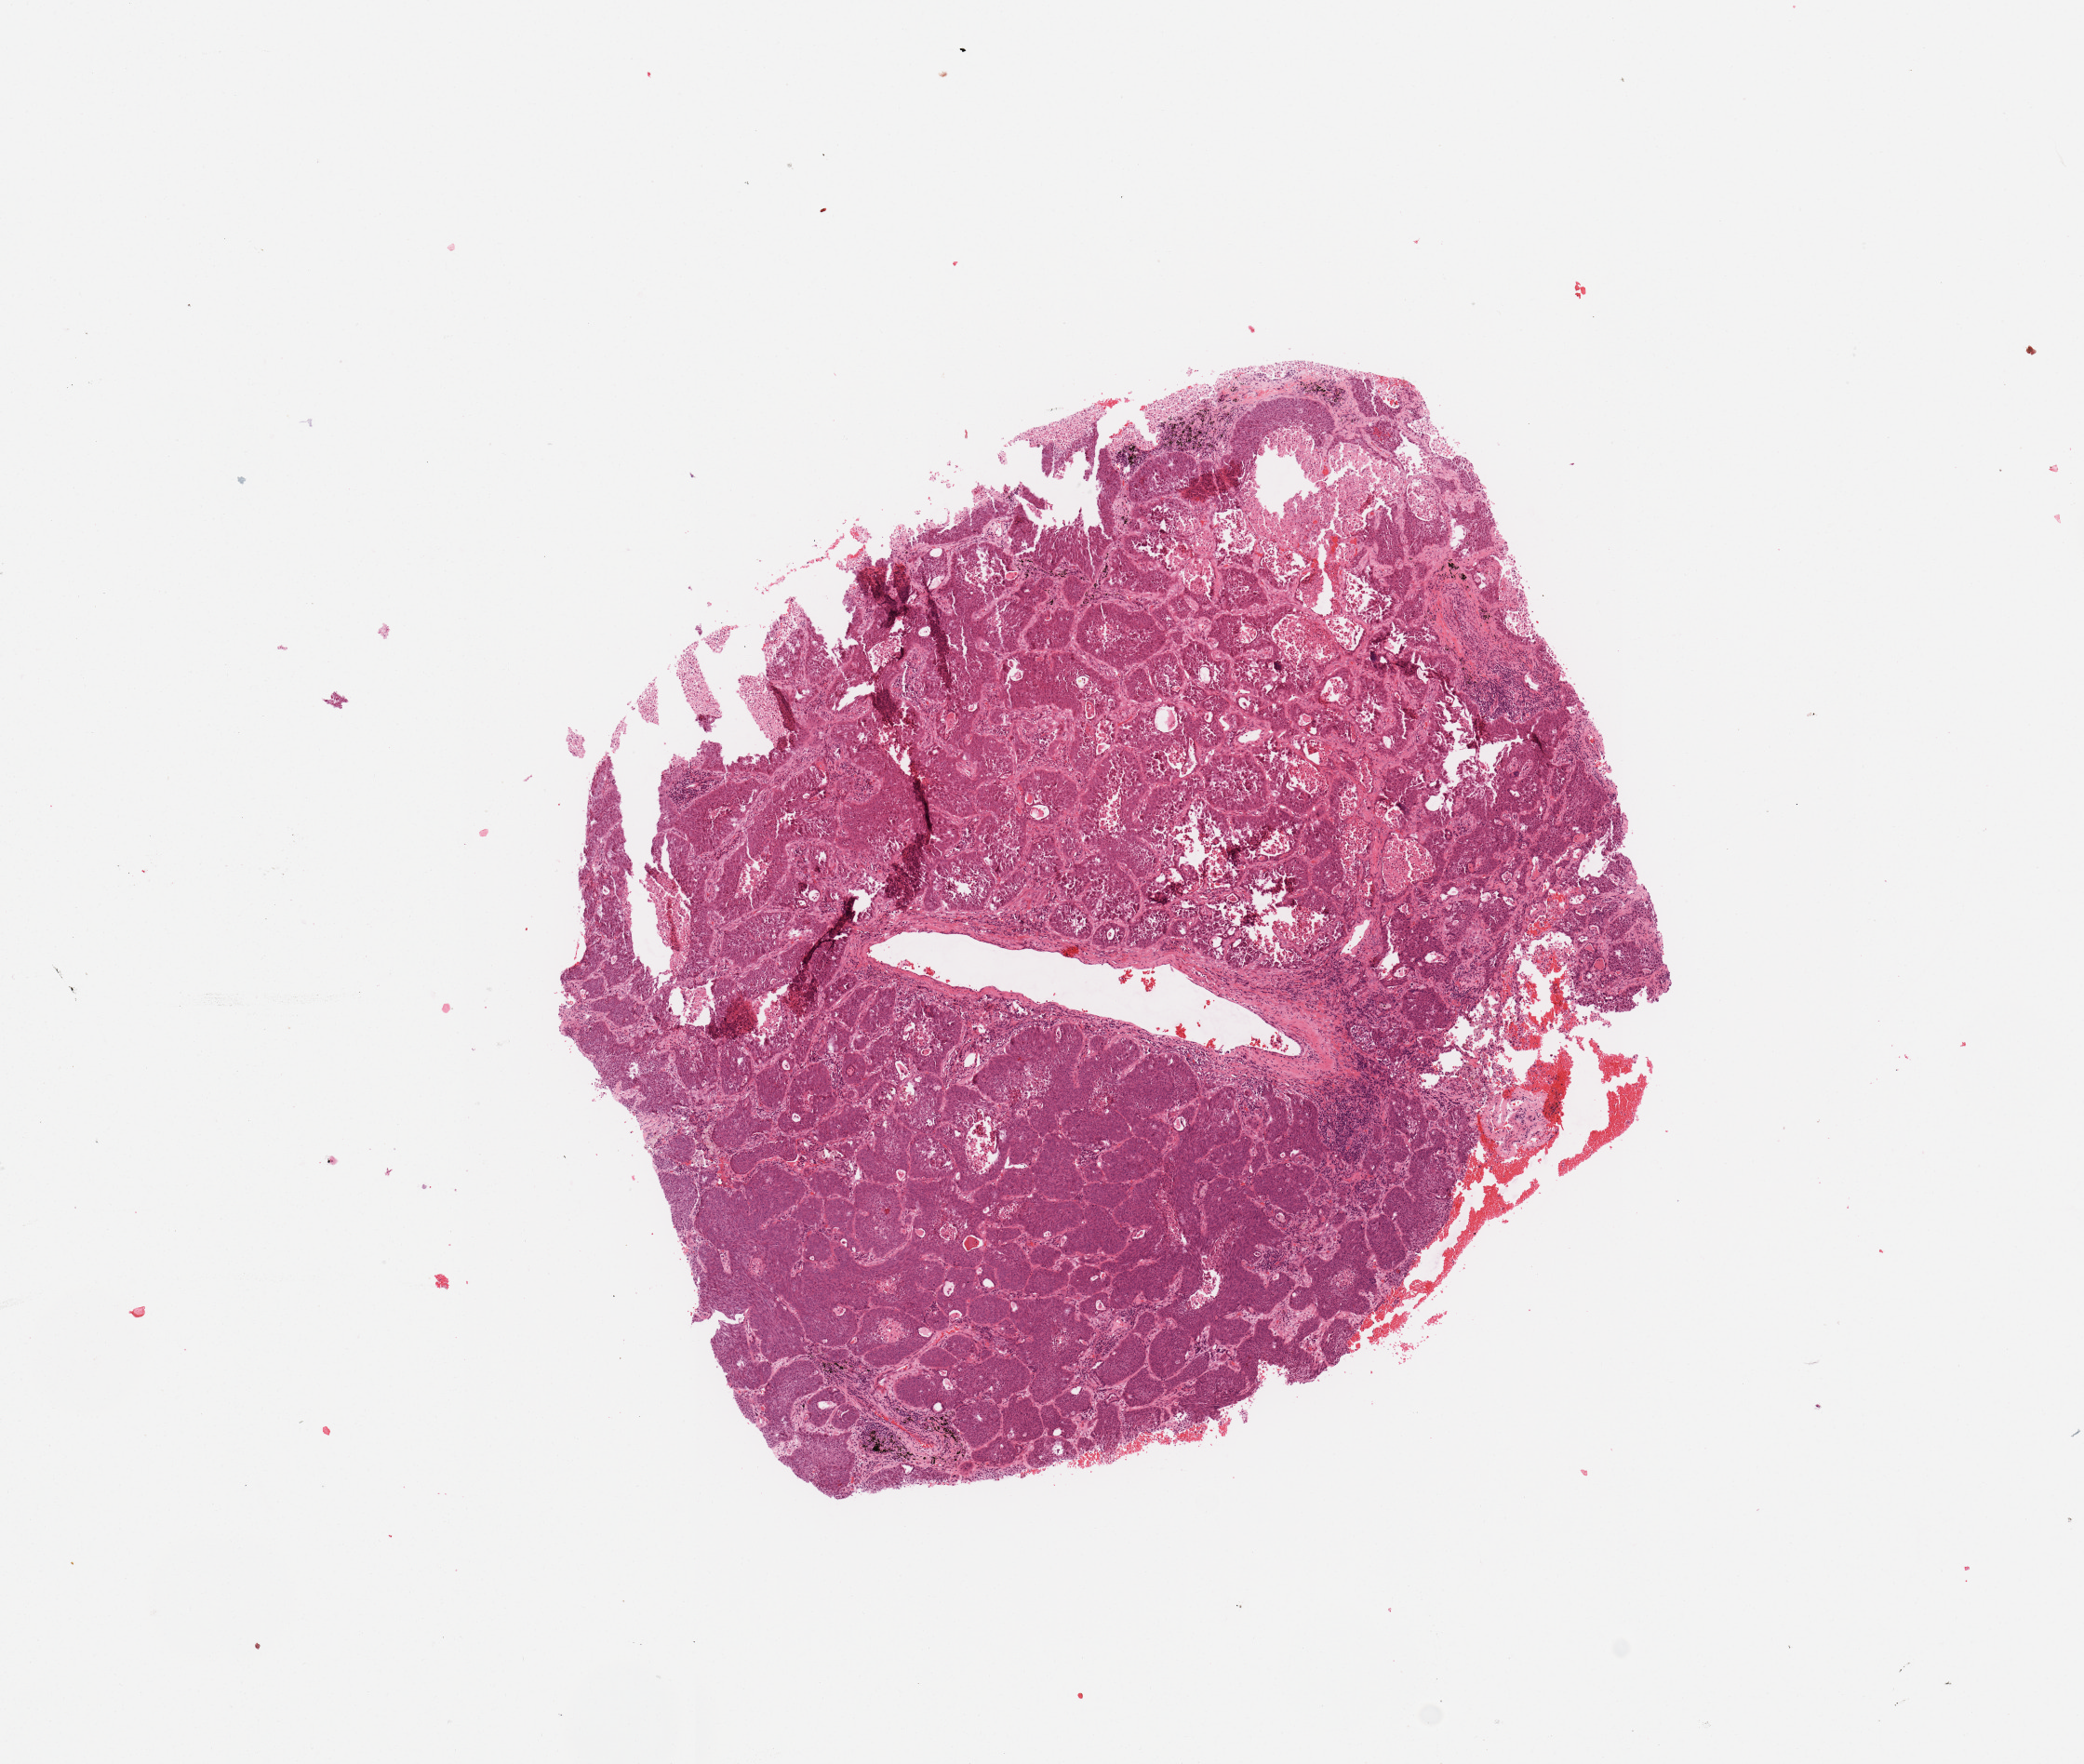
Whole-slide histology image, H&E — low-resolution overview of the scanned area, about 8.9 x 7.5 mm. Tumour tissue sample, sampled site: lung. Male, 62 y/o. Histologic grade: G2 (moderately differentiated). Slide review estimates, as recorded: tumour nuclei 80%, necrosis 5%.
- AJCC pathologic stage: IA3
- histologic diagnosis: Squamous cell carcinoma, NOS
- primary tumour site (as recorded): right upper lobe